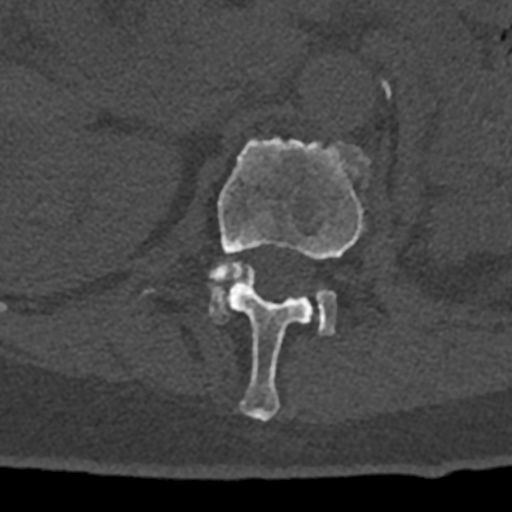
CT including the spine, one axial slice; slice 422 of 797 in the series (ordered by position); 120 kVp; bone window (W 1800 / L 400 HU); 0.5 mm slice thickness; 512 × 512 image matrix, field of view 160 × 160 mm. Male patient, age 74 years. From the clinical record (not read from this slice): primary cancer: renal; vertebrae with lytic lesions (as recorded): T10, L1, L2, L3, L4, L5.
Structures marked on this image (semi-automatic segmentation, software-assisted and operator-edited):
- L1 vertebra: bounding box <144,138,370,421> (left, top, right, bottom; pixels)
- L2 vertebra: <209,263,336,335>